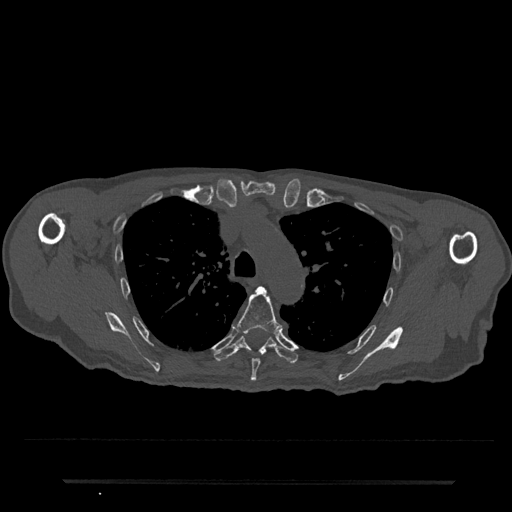
CT including the spine, one axial slice. Bone window (W 1800 / L 400 HU). 512 × 512 image matrix, field of view 427 × 427 mm. Male patient, age 74 years. From the clinical record (not read from this slice): primary cancer: prostate.
Outlined on this slice (semi-automatic segmentation, software-assisted and operator-edited):
- T5 vertebra: box from (x=237, y=286) to (x=282, y=382) px
- T6 vertebra: (x=214, y=334)–(x=298, y=364)